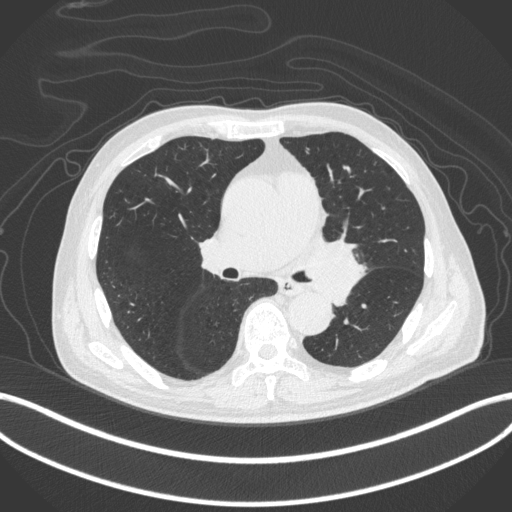
Chest CT, one axial slice; slice 246 of 420 in the series (ordered by position); reconstruction kernel B31f; 120 kVp; lung window (W 1500 / L -600 HU); 1 mm slice thickness; 512 × 512 image matrix. Male patient, age 77 years. Case-level facts recorded for this patient, not image findings: clinical TNM (as recorded): T3 N1 M0.
Outlined on this slice (bounding box drawn by a radiologist):
- lung tumour (recorded histology: adenocarcinoma): bounding box (x1, y1, x2, y2) in pixels: (302, 237, 366, 313)